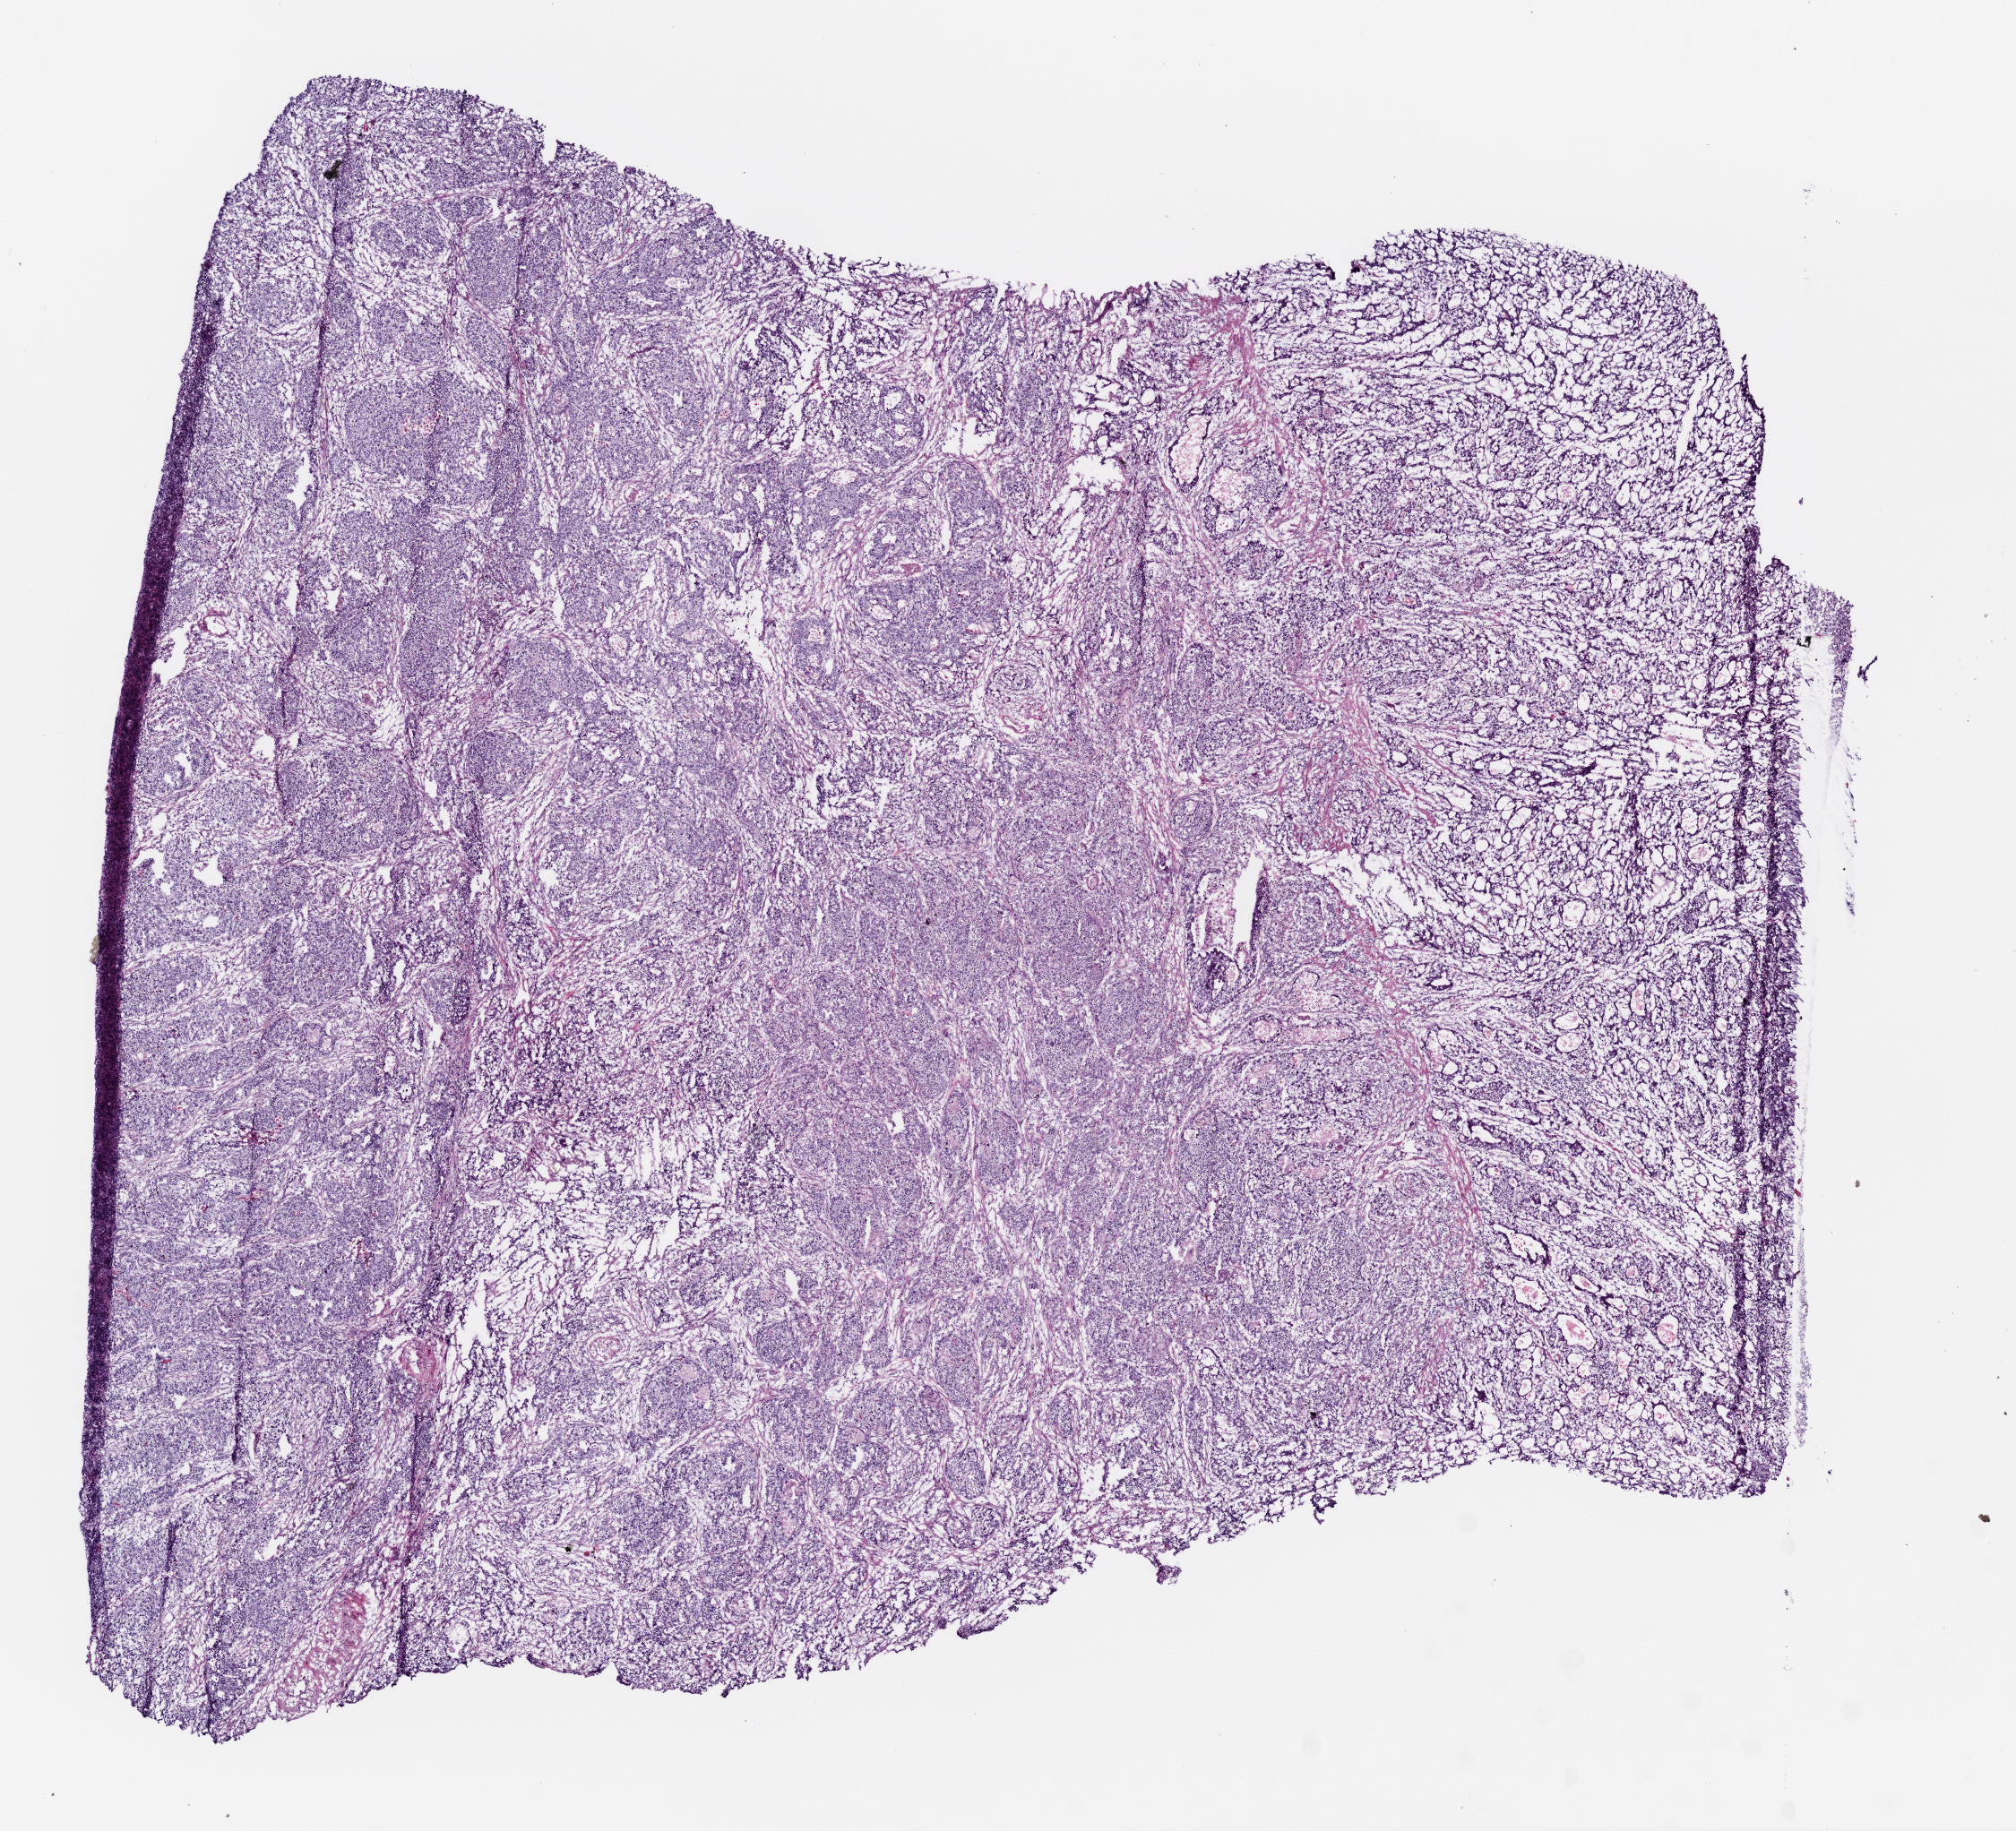
Whole-slide histology image, Hematoxylin and eosin (H&E) stained, low-resolution overview of the scanned area, about 9.0 x 8.2 mm. Frozen section. Primary tumour sample from the stomach. Male, age 79 years at initial diagnosis. Histologic grade: G2 (moderately differentiated). Slide review estimates, as recorded: tumour cells 96%, tumour nuclei 72%, normal cells 0%, stromal cells 2%, necrosis 2%. Inflammatory infiltration, as recorded: lymphocyte infiltration 2%, neutrophil infiltration 24%.
- TNM: T3 N2 M0
- AJCC pathologic stage: IIIB
- diagnosis: Adenocarcinoma, NOS (gastric antrum)